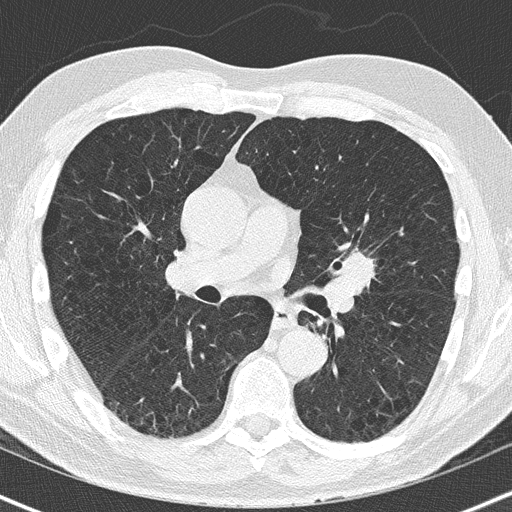
Axial slice from a low-dose chest CT screening exam, baseline annual screen, lung window (W 1500 / L -600 HU), 2 mm slice thickness, lung (sharp) reconstruction kernel (B50f), 120 kVp, slice 76 of 163 in the series, 512 × 512 image matrix, field of view 320 × 320 mm. Male participant, aged 63 years at enrolment.
• Expert reader's lesion annotation, bounding box [x1, y1, x2, y2] px = [333, 253, 379, 291].
• The screening reader recorded 2 non-calcified nodules or masses ≥4 mm on this exam; which of them this box marks is not recorded.
• Lung cancer was diagnosed 32 days after this screen: squamous cell carcinoma, NOS, left upper lobe, moderately differentiated (G2), stage IA (AJCC 6th edition), 23 mm at pathology.